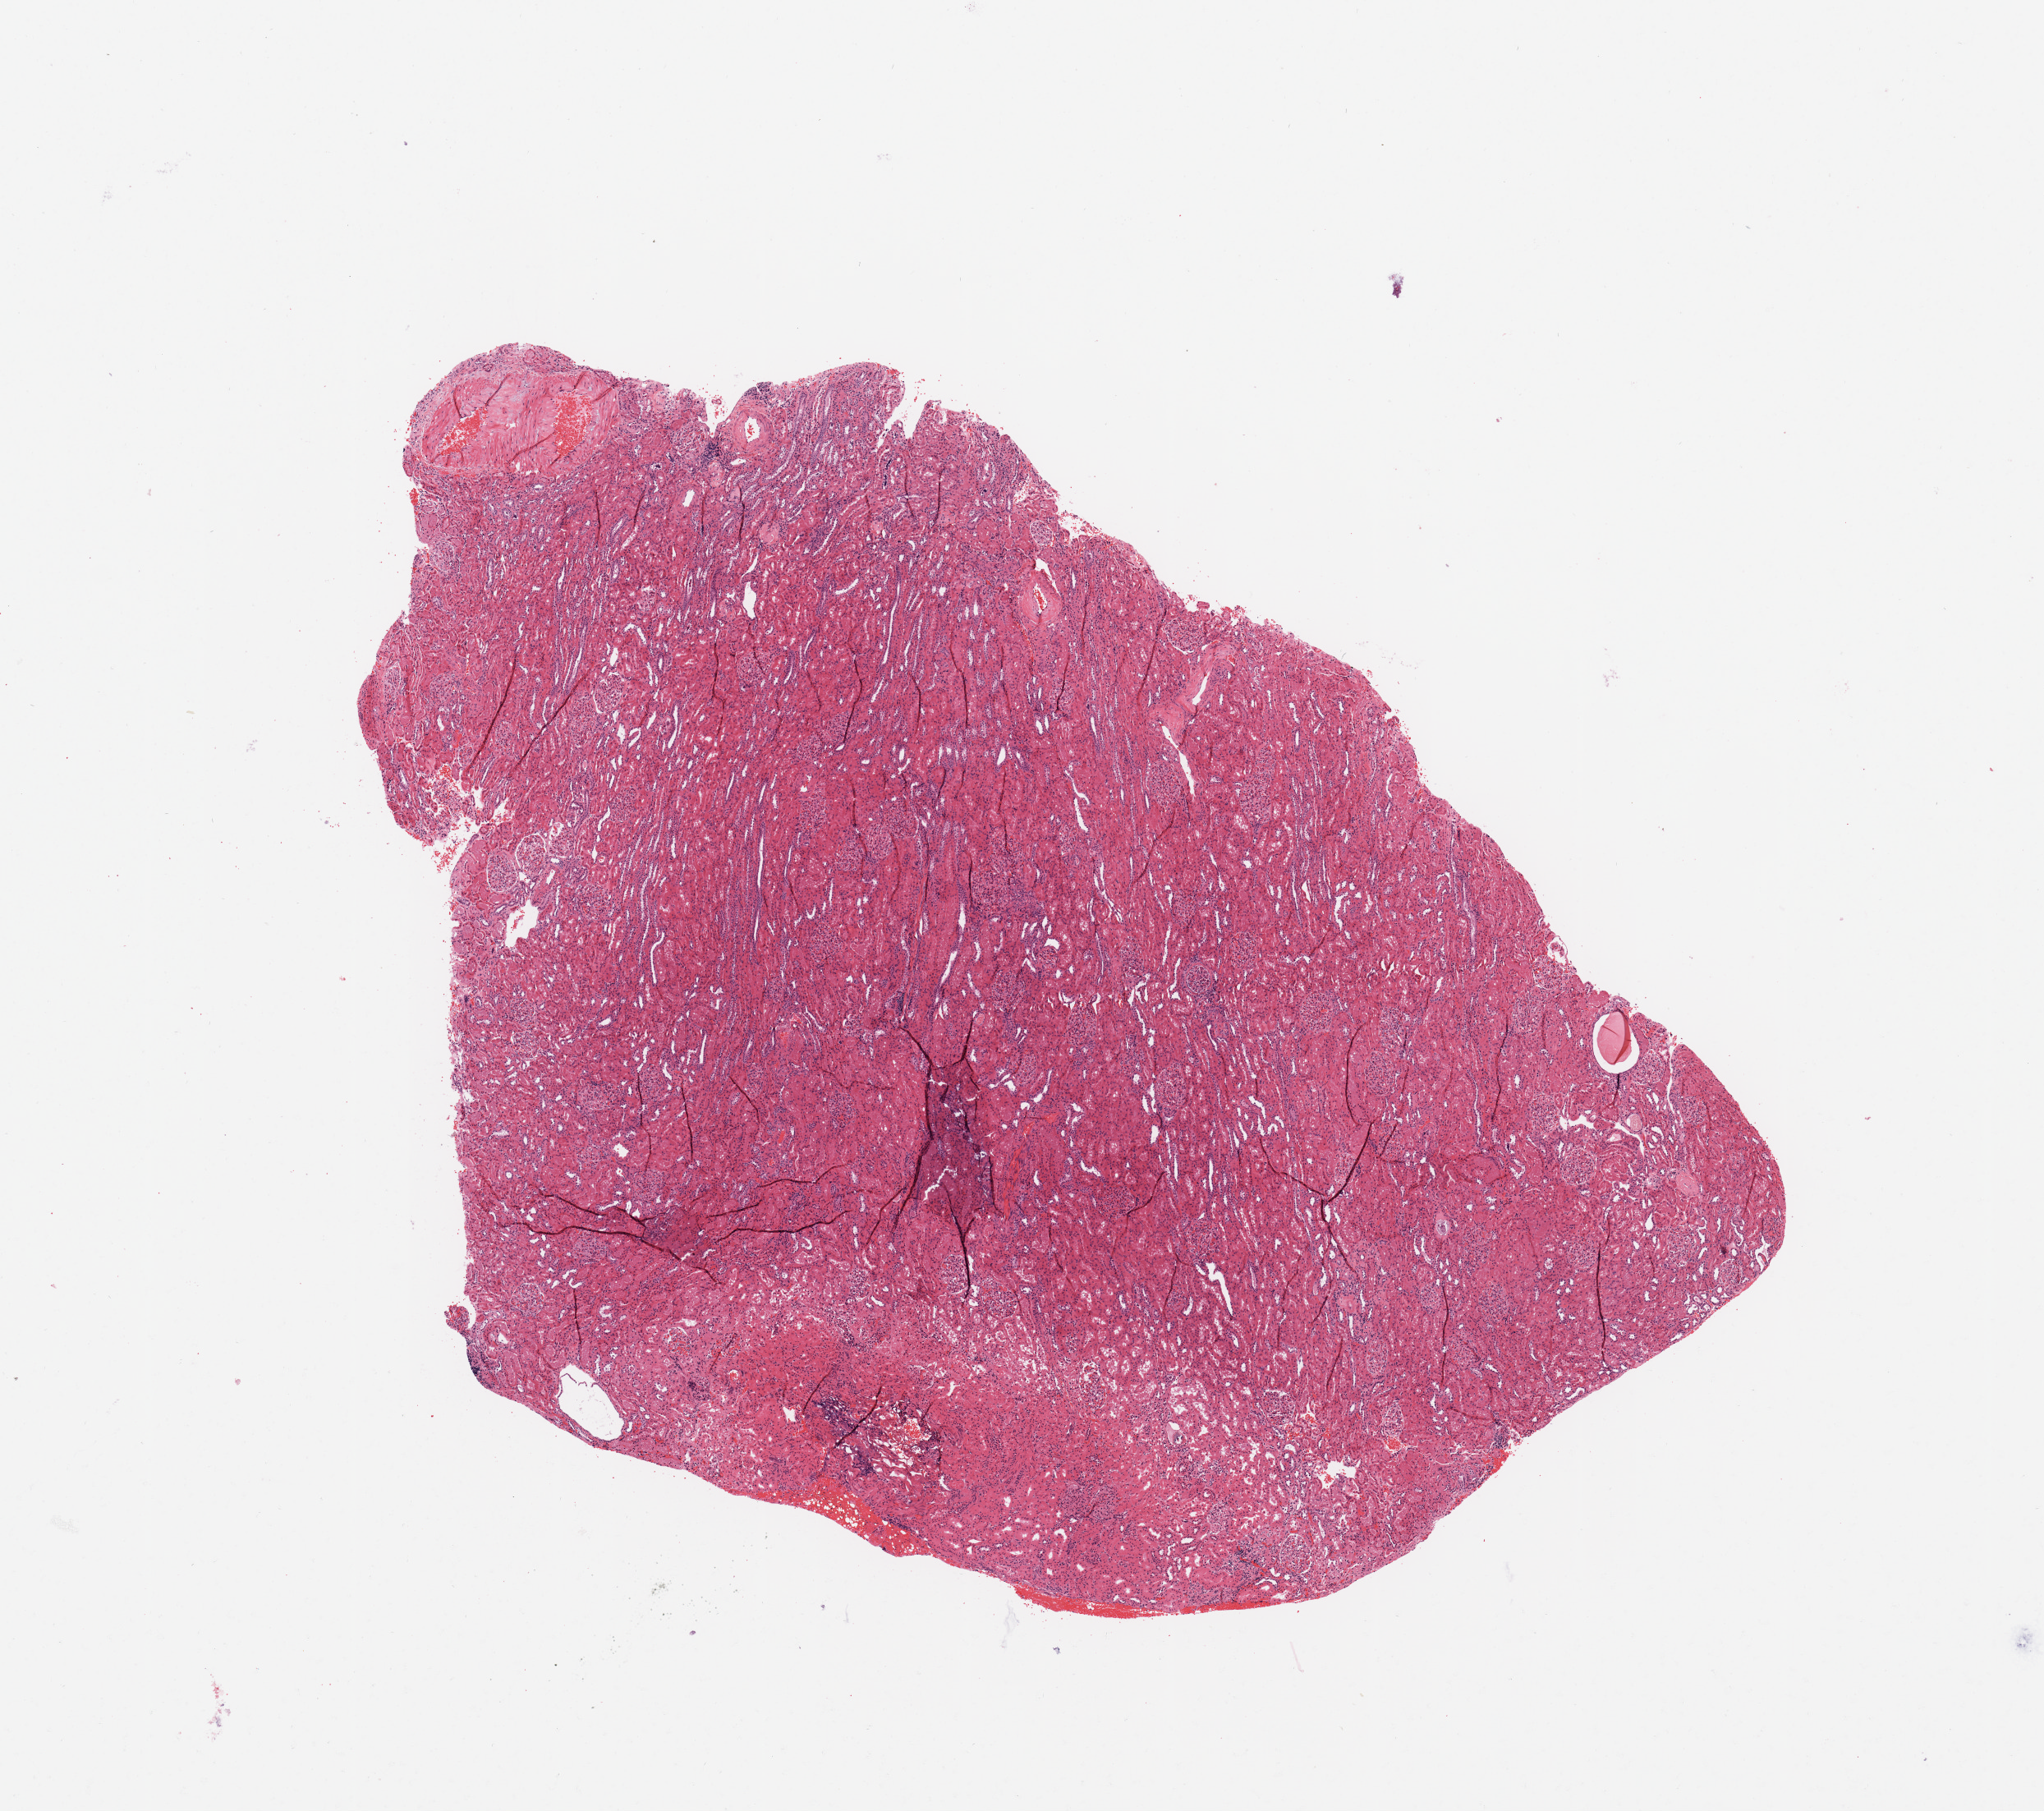
H&E whole-slide image — low-resolution overview of the scanned area, about 9.8 x 8.7 mm, normal (non-tumour) tissue sample, sampled site: kidney. Patient: female, age 61 years.
This section: normal (non-tumour) tissue from the same patient. Patient diagnosis: Renal cell carcinoma, NOS.